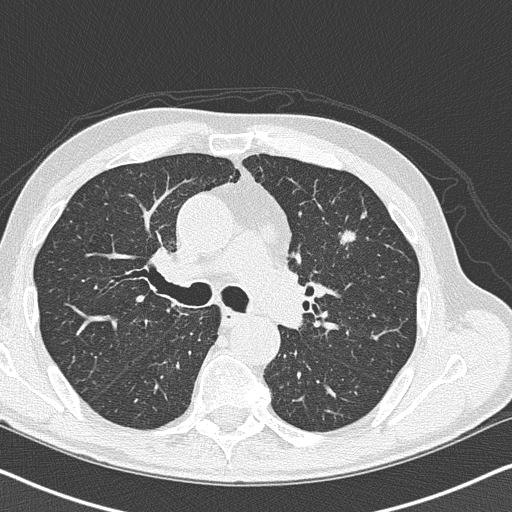
Low-dose screening chest CT, one axial slice; position 101 of 158 along the scan axis; reconstruction kernel B50f; 120 kVp; lung window (W 1500 / L -600 HU); 2 mm slice thickness; 512 × 512 image matrix, field of view 330 × 330 mm.
Structures marked on this image (expert manual segmentation):
- lesion 1 (tumor, upper lobe of left lung): box from (x=340, y=231) to (x=357, y=245) px